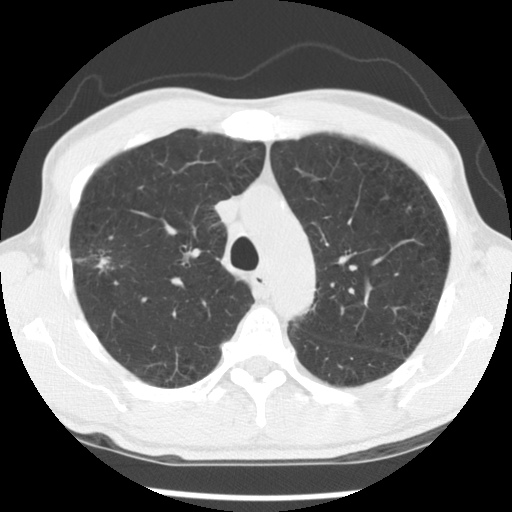
Low-dose screening chest CT, one axial slice. Slice 95 of 138 in the series (ordered by position). 140 kVp. Lung window (W 1500 / L -600 HU). 512 × 512 image matrix, field of view 320 × 320 mm.
Outlined on this slice (outlined manually by an expert reader):
- lesion 1 (tumor, upper lobe of right lung): bounding box (x1, y1, x2, y2) in pixels: (96, 257, 109, 271)